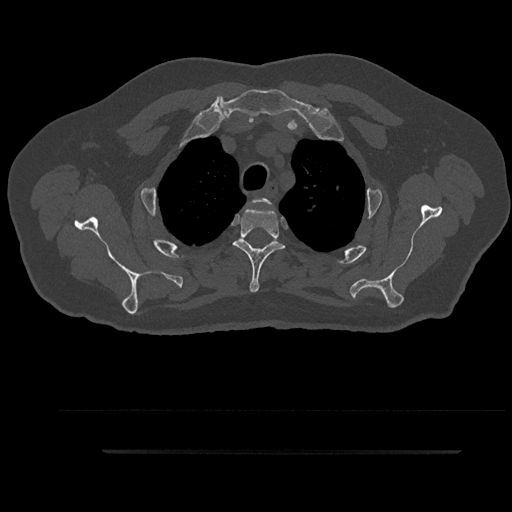
CT including the spine, one axial slice; position 715 of 797 along the scan axis; 120 kVp; bone window (W 1800 / L 400 HU); 0.5 mm slice thickness; 512 × 512 image matrix, field of view 432 × 432 mm. Patient: male, 63 years. Case-level facts recorded for this patient, not image findings: primary cancer: renal; vertebrae with lytic lesions (as recorded): T8.
Structures marked on this image (semi-automatically segmented with operator editing):
- T2 vertebra: bounding box (x1, y1, x2, y2) in pixels: (253, 198, 272, 206)
- T3 vertebra: (233, 207, 285, 293)